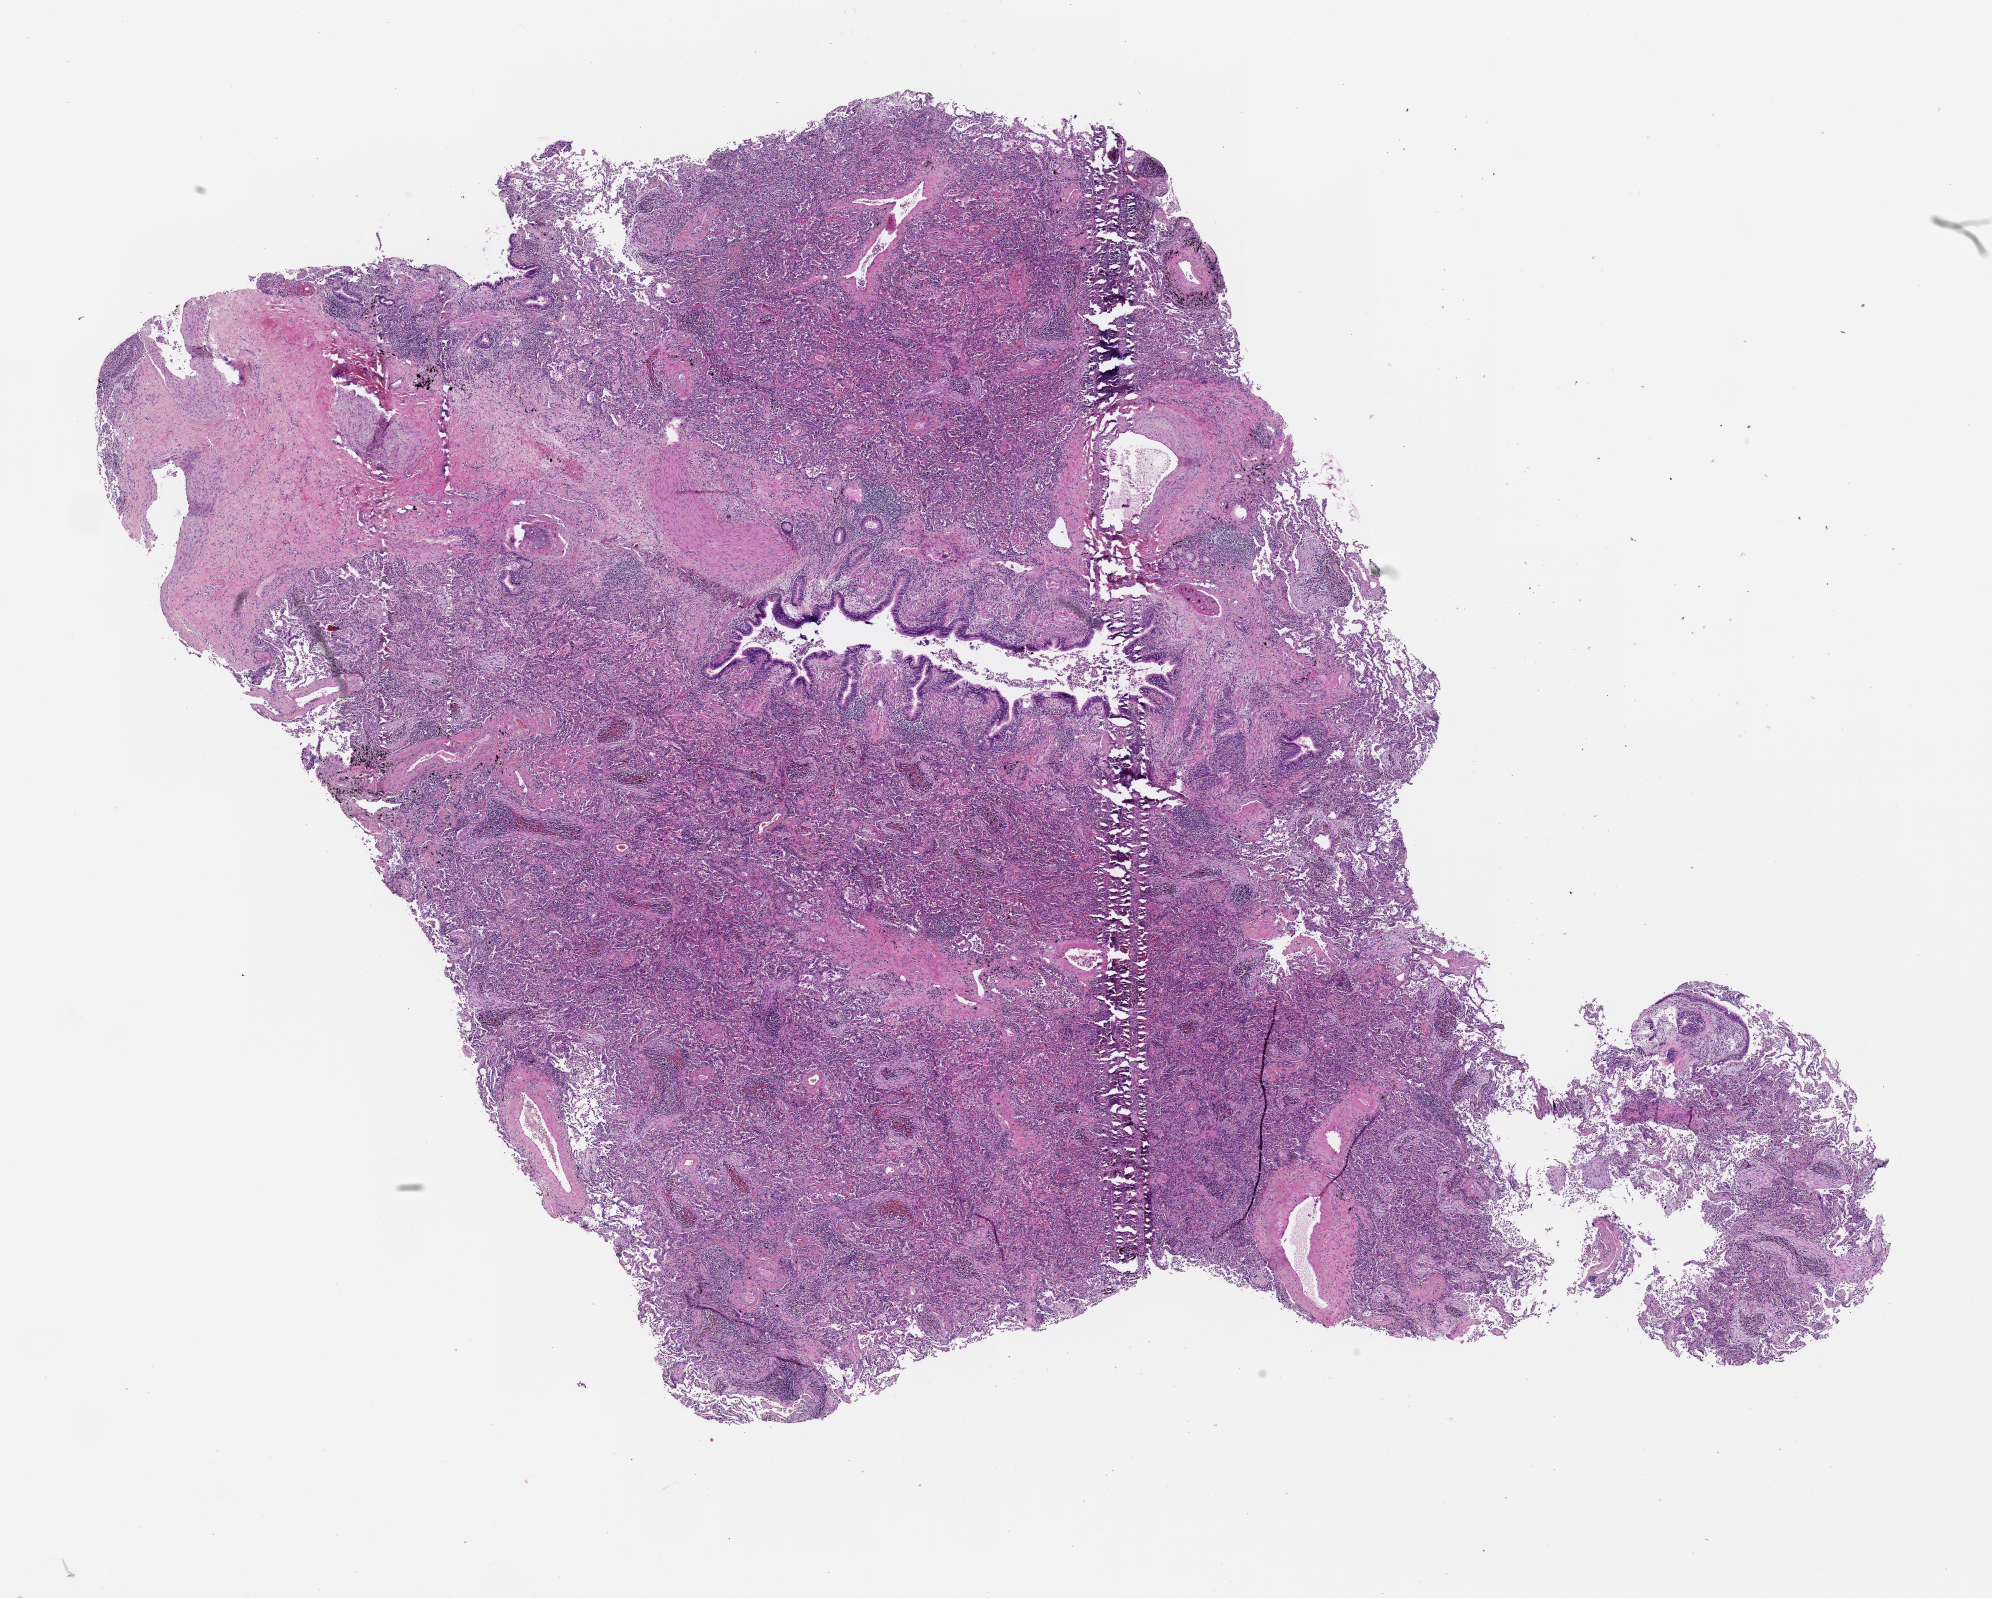
H&E-stained whole-slide image, low-resolution overview of the scanned area, about 16.0 x 12.9 mm (slide scanned at 20x). Normal (non-tumour) tissue sample, lung. 64-year-old male patient.
* this section: normal (non-tumour) tissue from the same patient
* patient diagnosis (cohort enrolment): squamous cell carcinoma (lung)